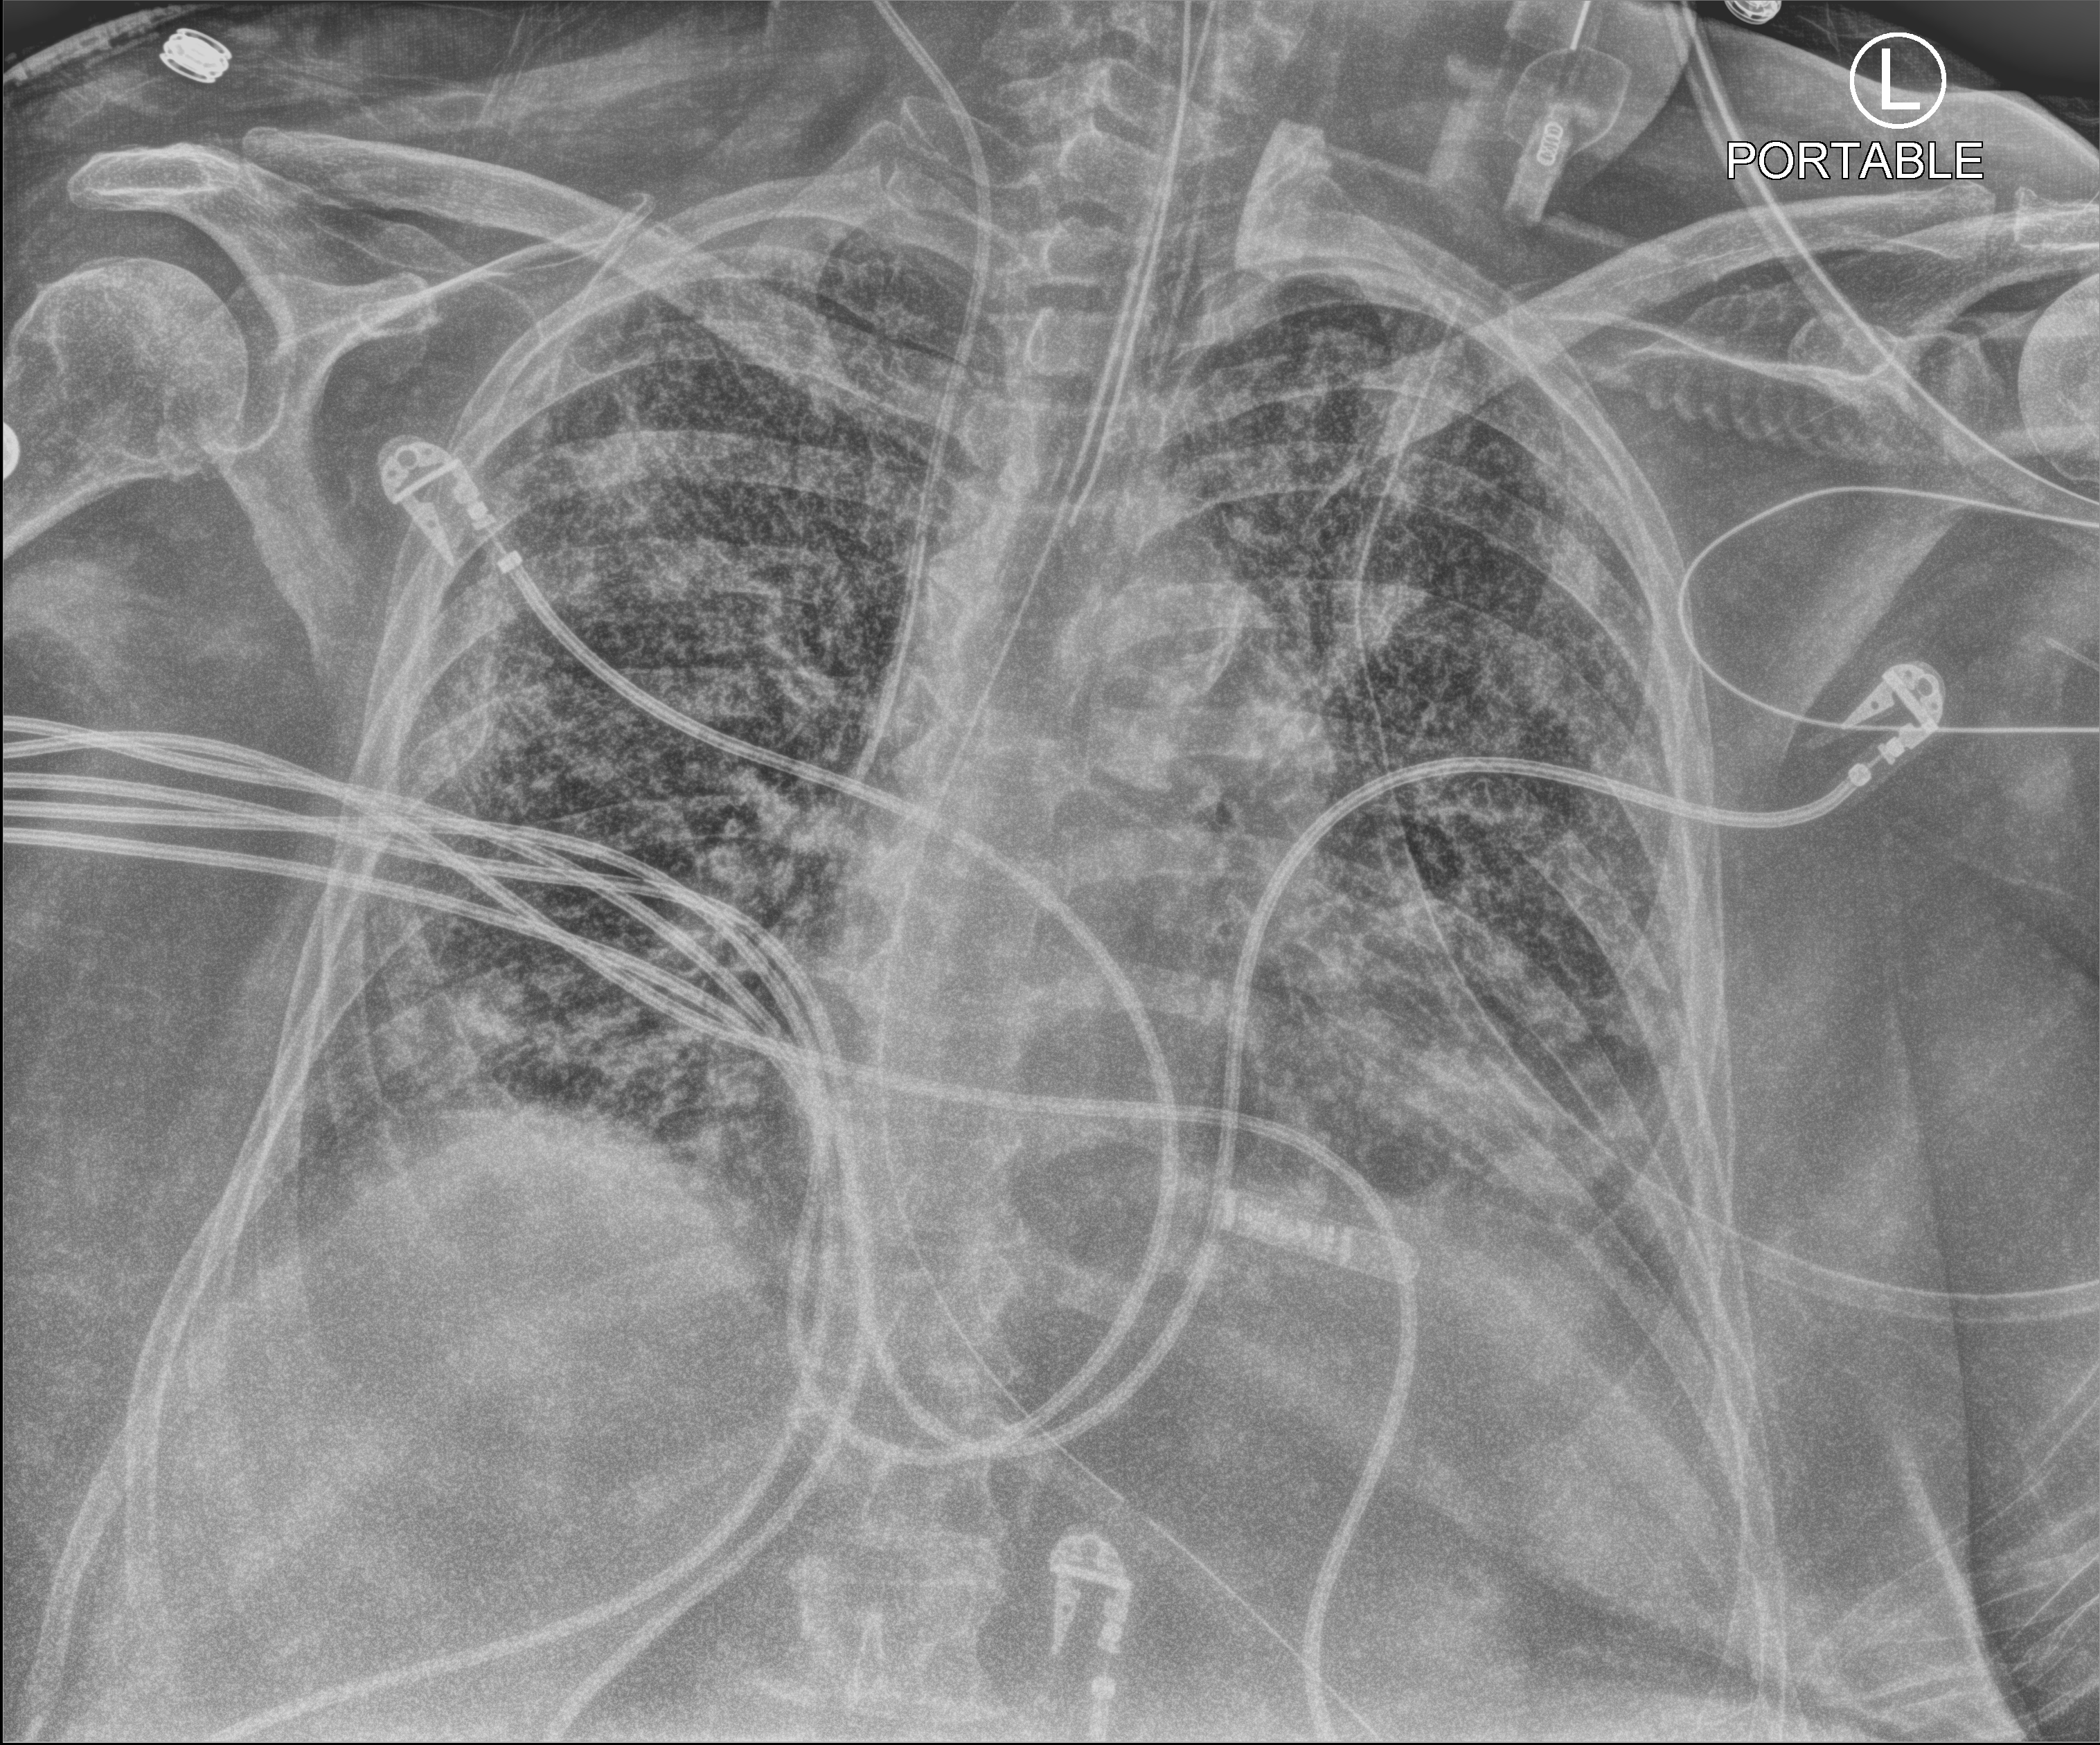
Portable chest radiograph; anteroposterior (AP) projection. Patient hospitalised with COVID-19; female, aged 60–74 years.
Hospital-stay facts (about this admission, not read from this image; timing relative to this image not recorded): COPD (admission record): no; mechanically ventilated during this hospital stay: yes.